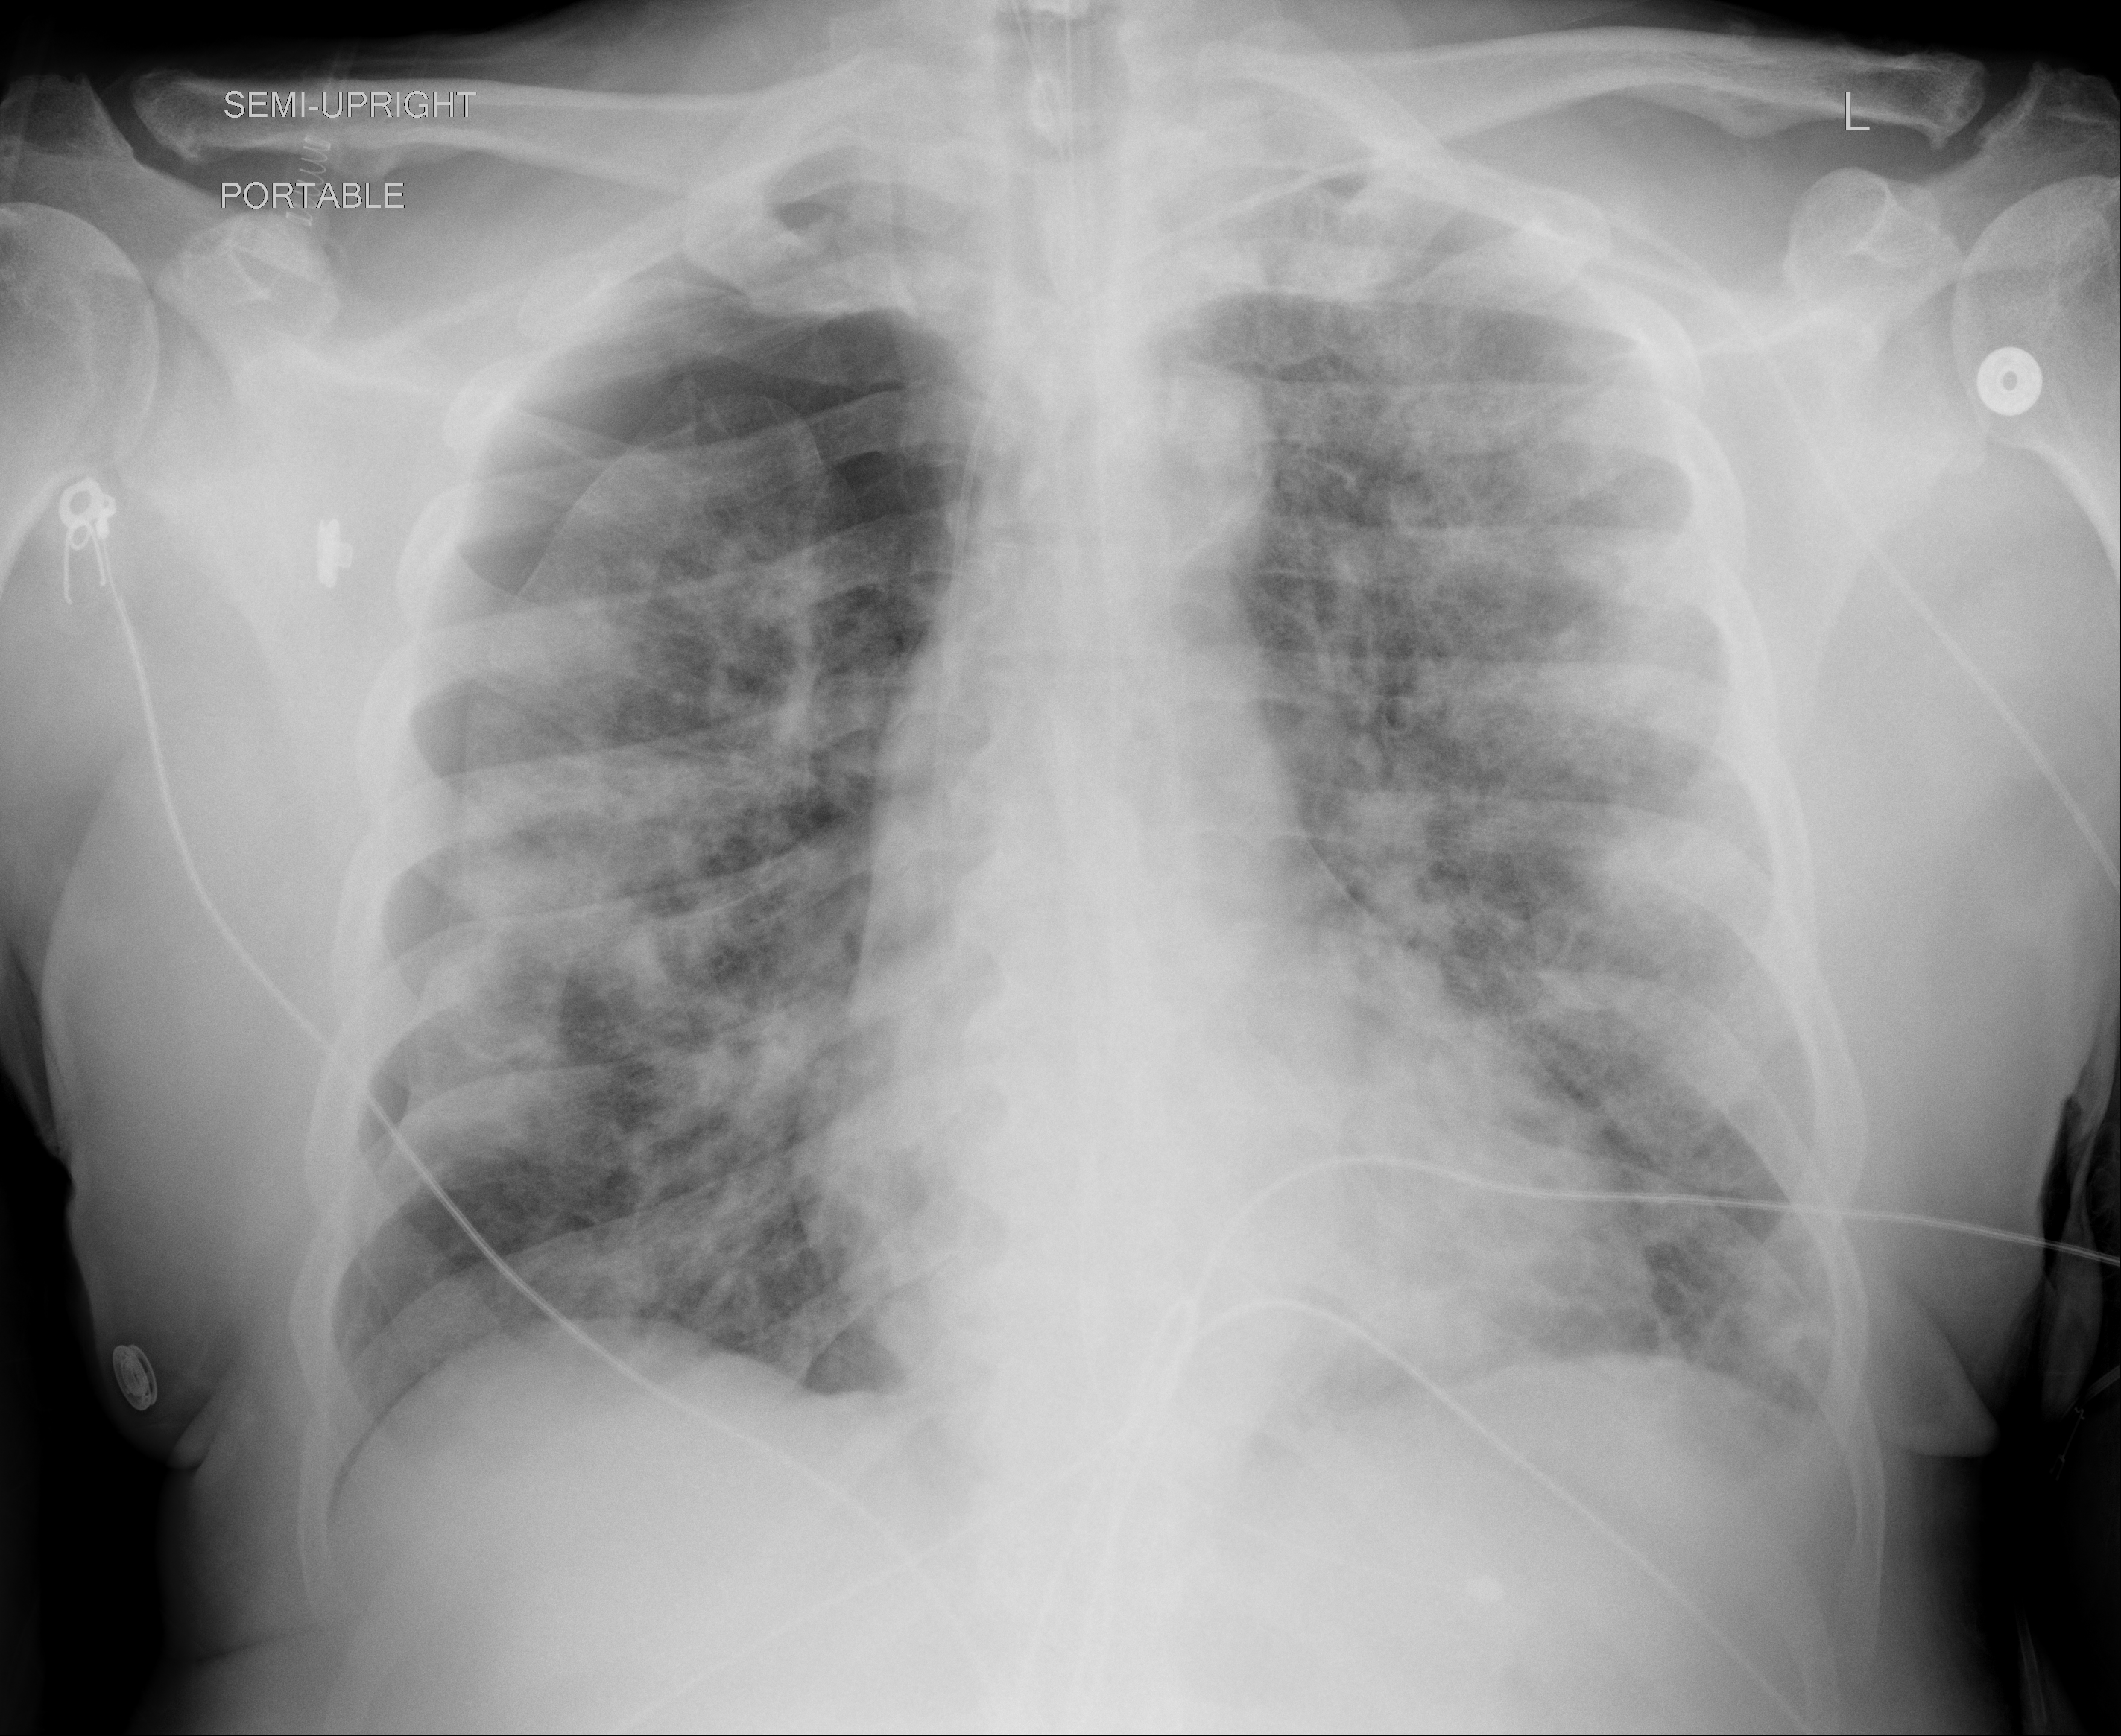
Chest X-ray (portable), AP projection. Male patient, age 64 years; imaged 8 days after the COVID-19 diagnosis.
Radiologist's key findings for this exam: Interval development of moderate-sized right pneumothorax. Stable patchy opacities throughout both lungs.